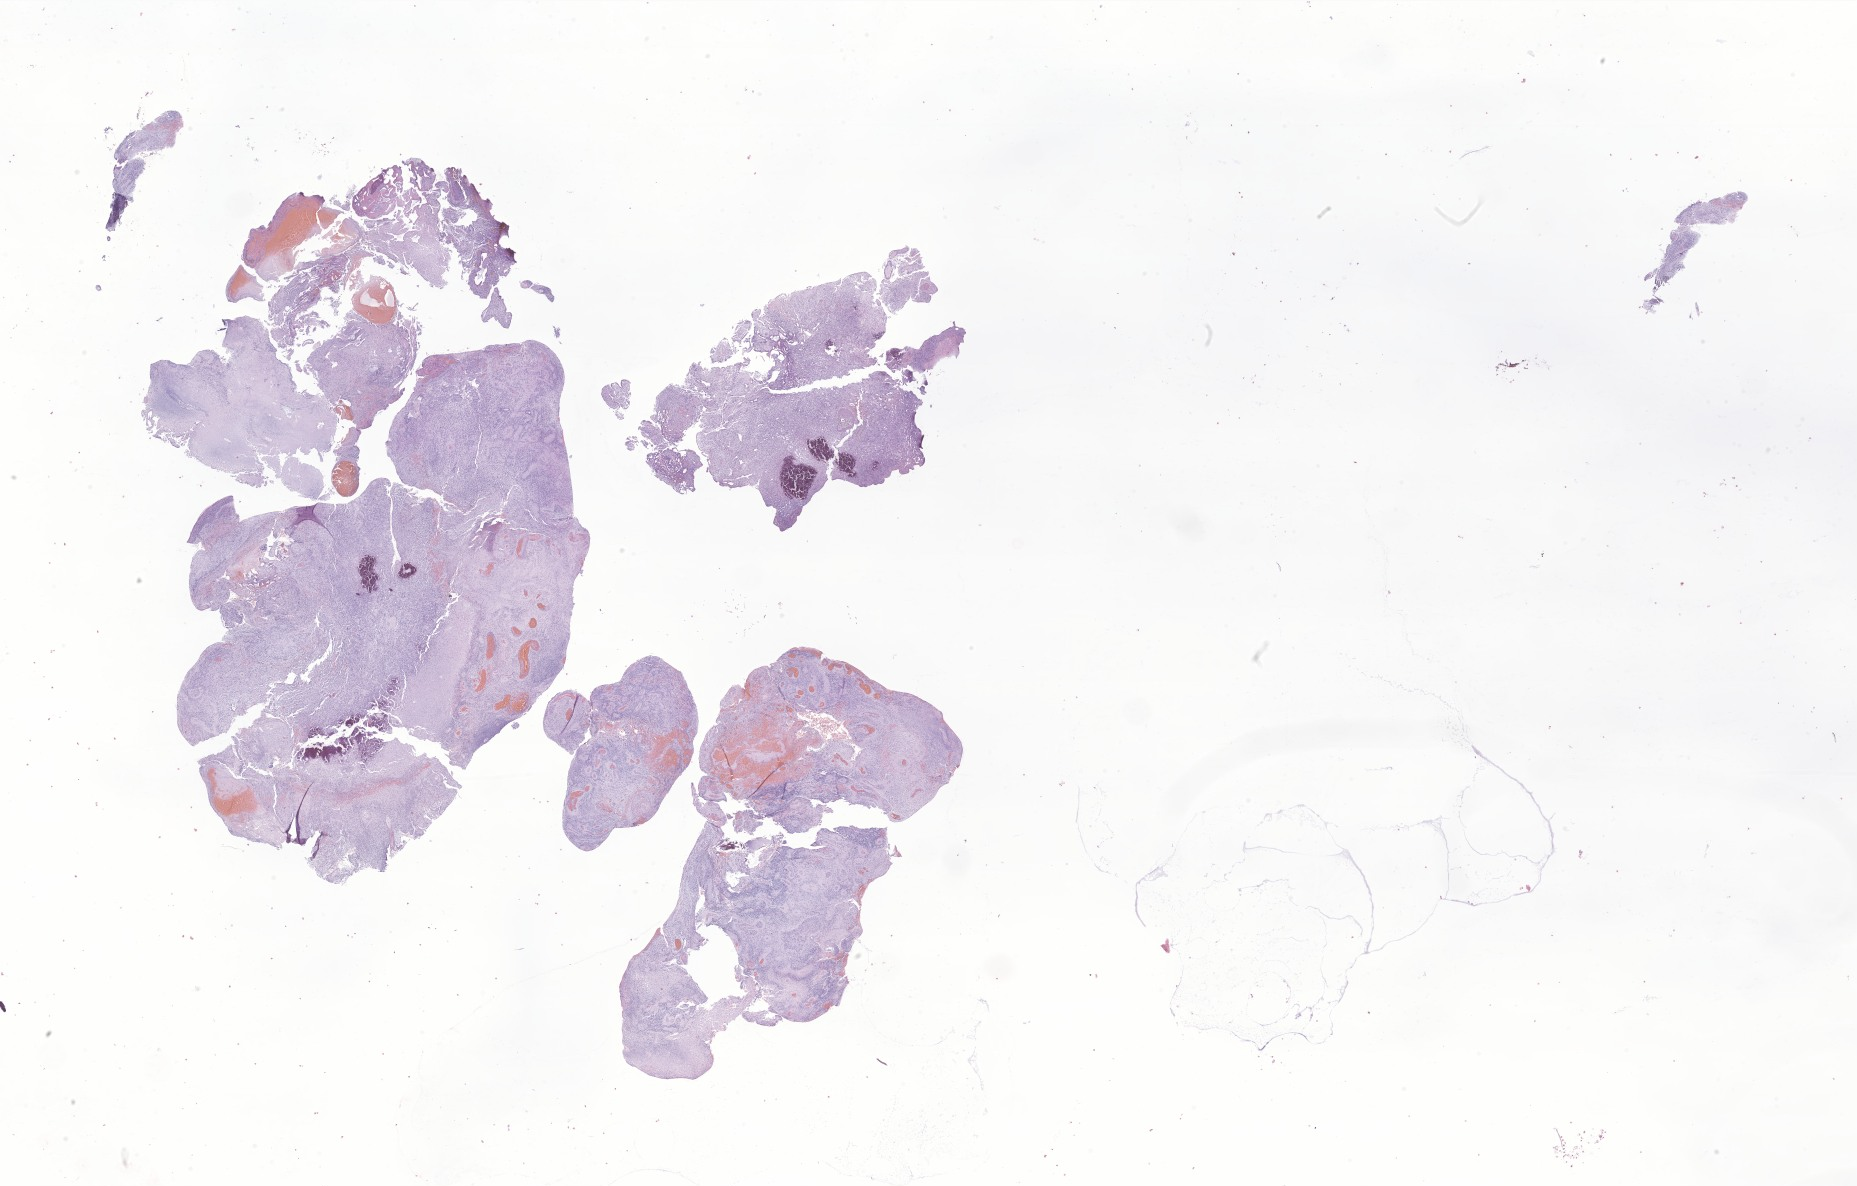
Digitized H&E-stained section of tumor tissue from the cerebellum — a low-resolution overview of the entire scanned area, about 31.3 x 20.0 mm, formalin-fixed paraffin-embedded section. Patient: female, age 427 days (about 1.2 years).
- recorded diagnosis: Neoplasm, uncertain whether benign or malignant